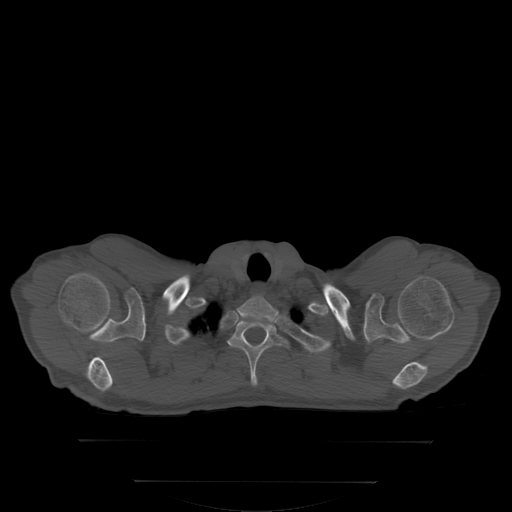
CT including the spine, one axial slice. Slice 289 of 350 in the series (ordered by position). Bone window (W 1800 / L 400 HU). 2.5 mm slice thickness. 512 × 512 image matrix. Patient: male, 58 years. Case-level facts recorded for this patient, not image findings: primary cancer: prostate; vertebrae with lytic lesions (as recorded): L1.
Annotated regions visible in this slice (semi-automatic segmentation, software-assisted and operator-edited):
- T1 vertebra: bounding box <228,321,290,385> (left, top, right, bottom; pixels)